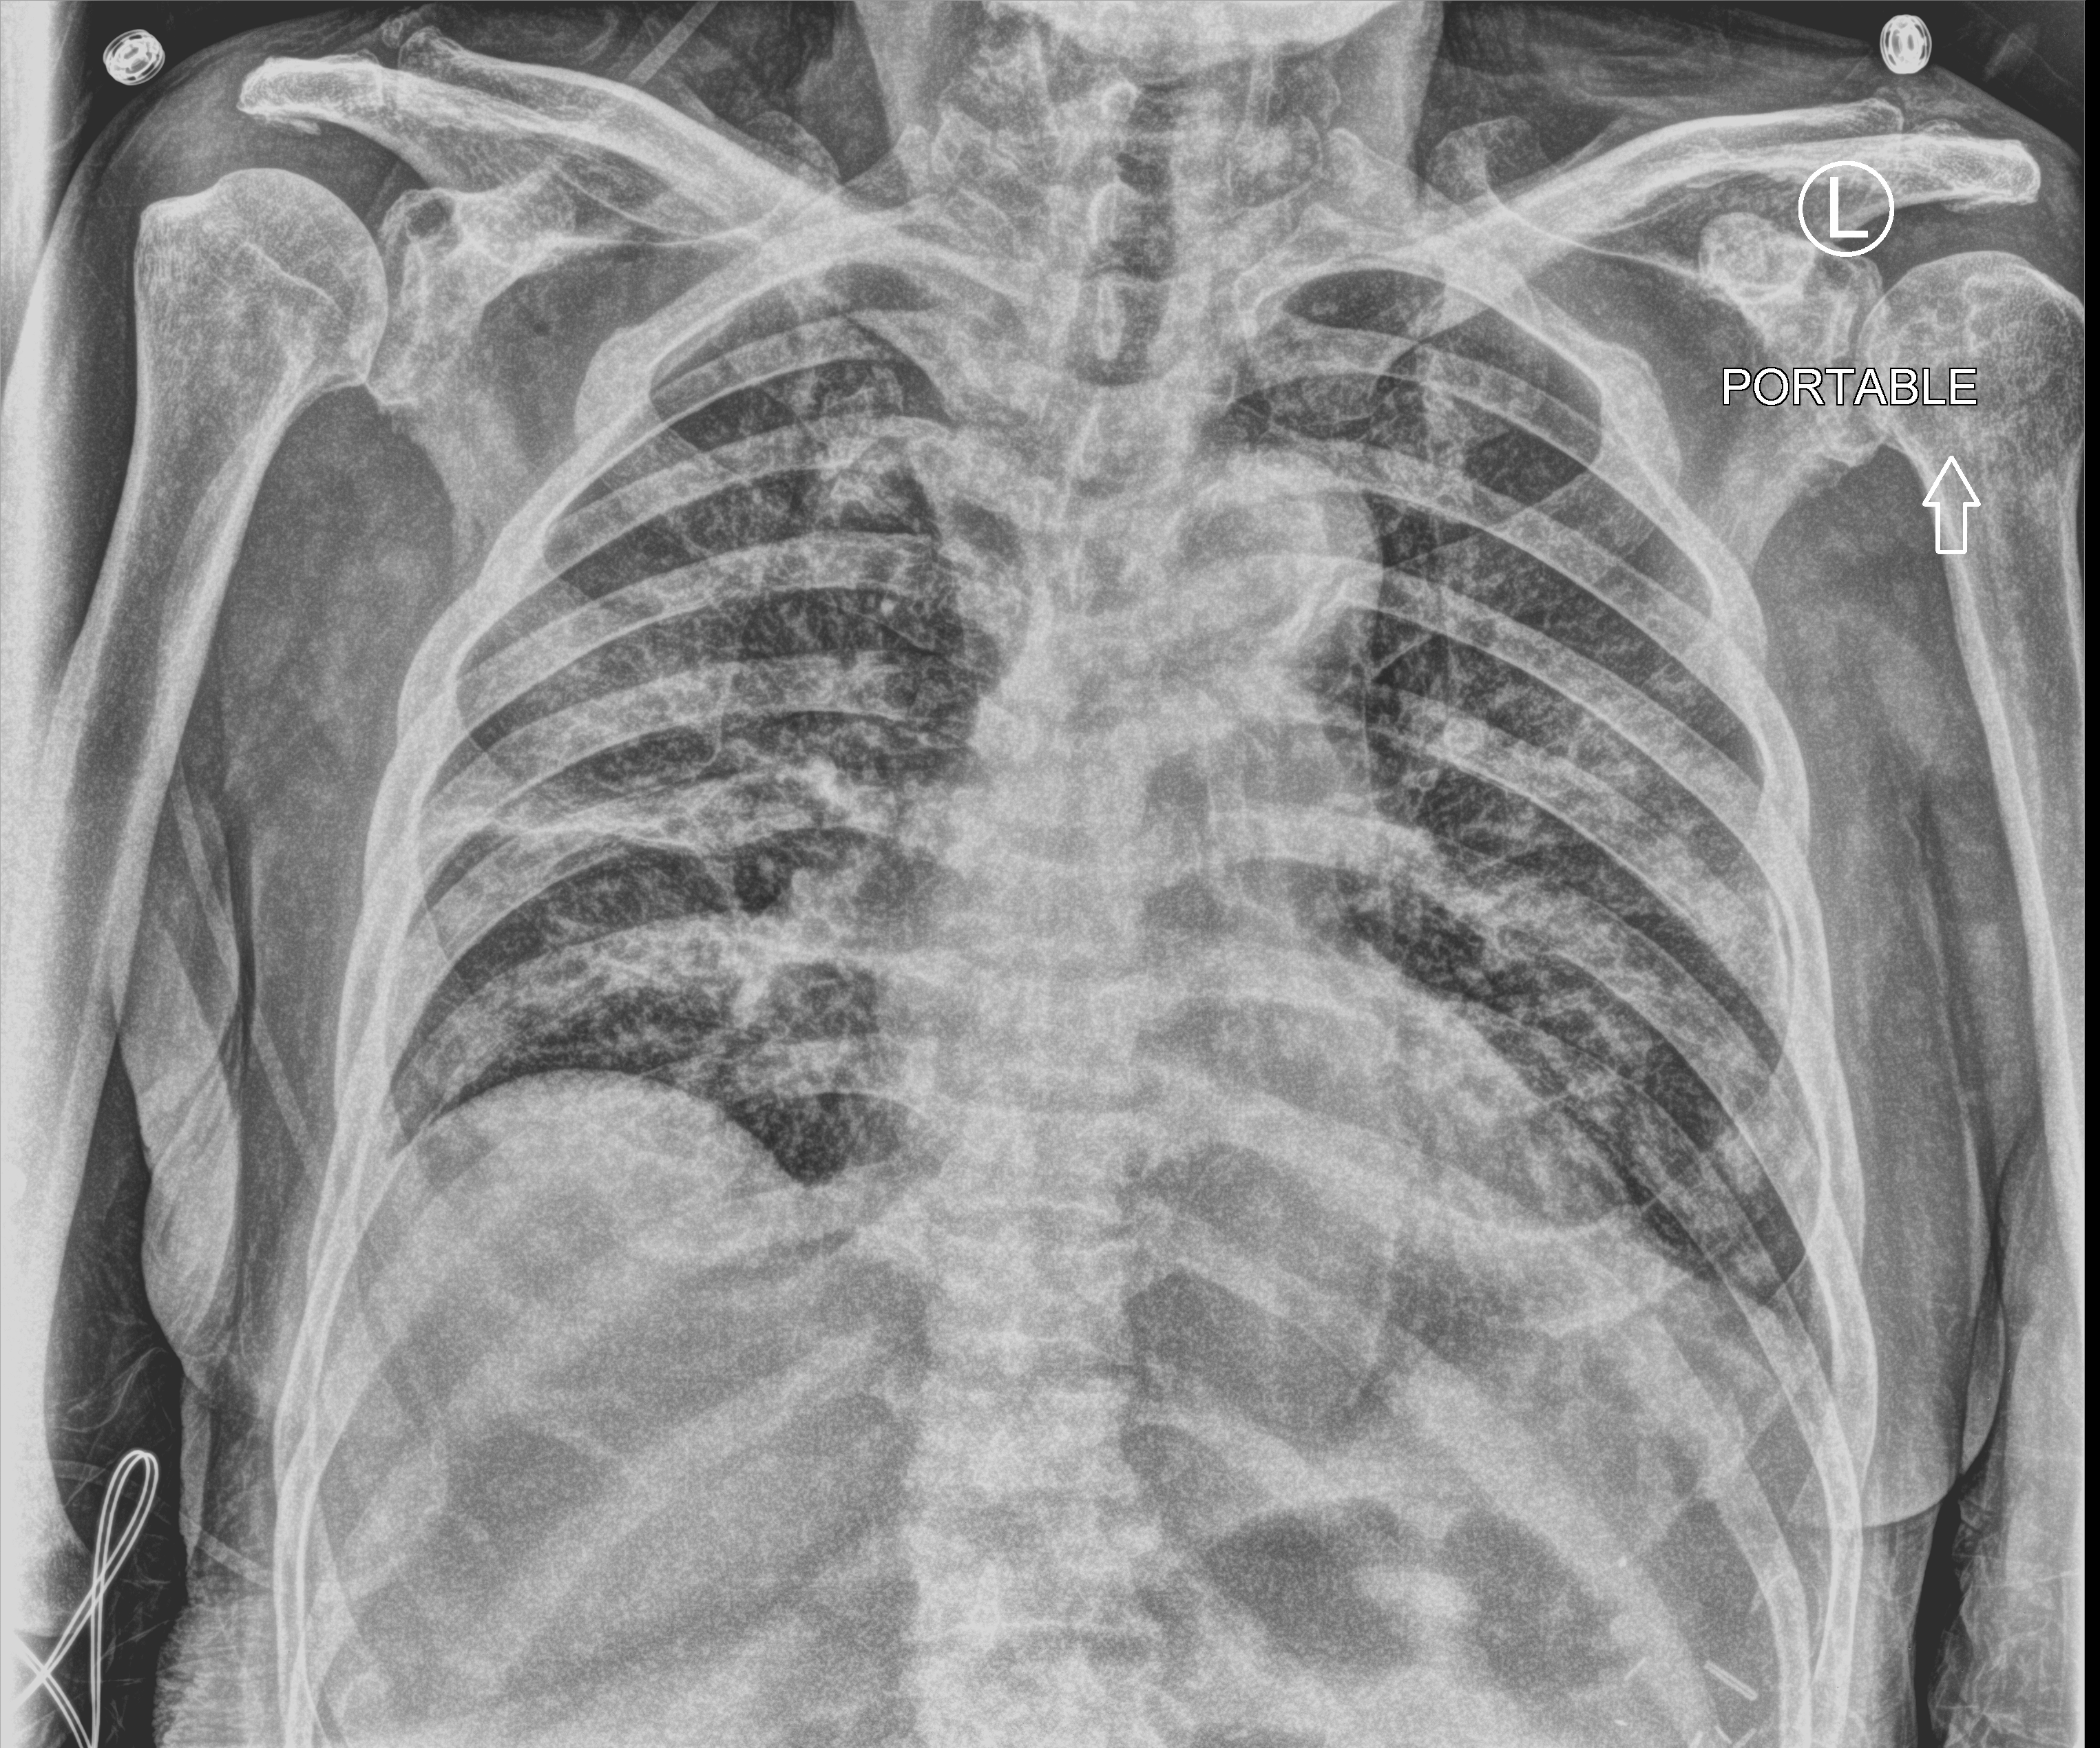
Portable chest radiograph. Male patient hospitalised with COVID-19, age 75–90 years.
From the hospital-stay record, not from the radiograph (when in the stay this image was taken is not recorded):
- mechanically ventilated during this hospital stay: no
- admitted to intensive care during this hospital stay: no
- length of hospital stay: 12 days